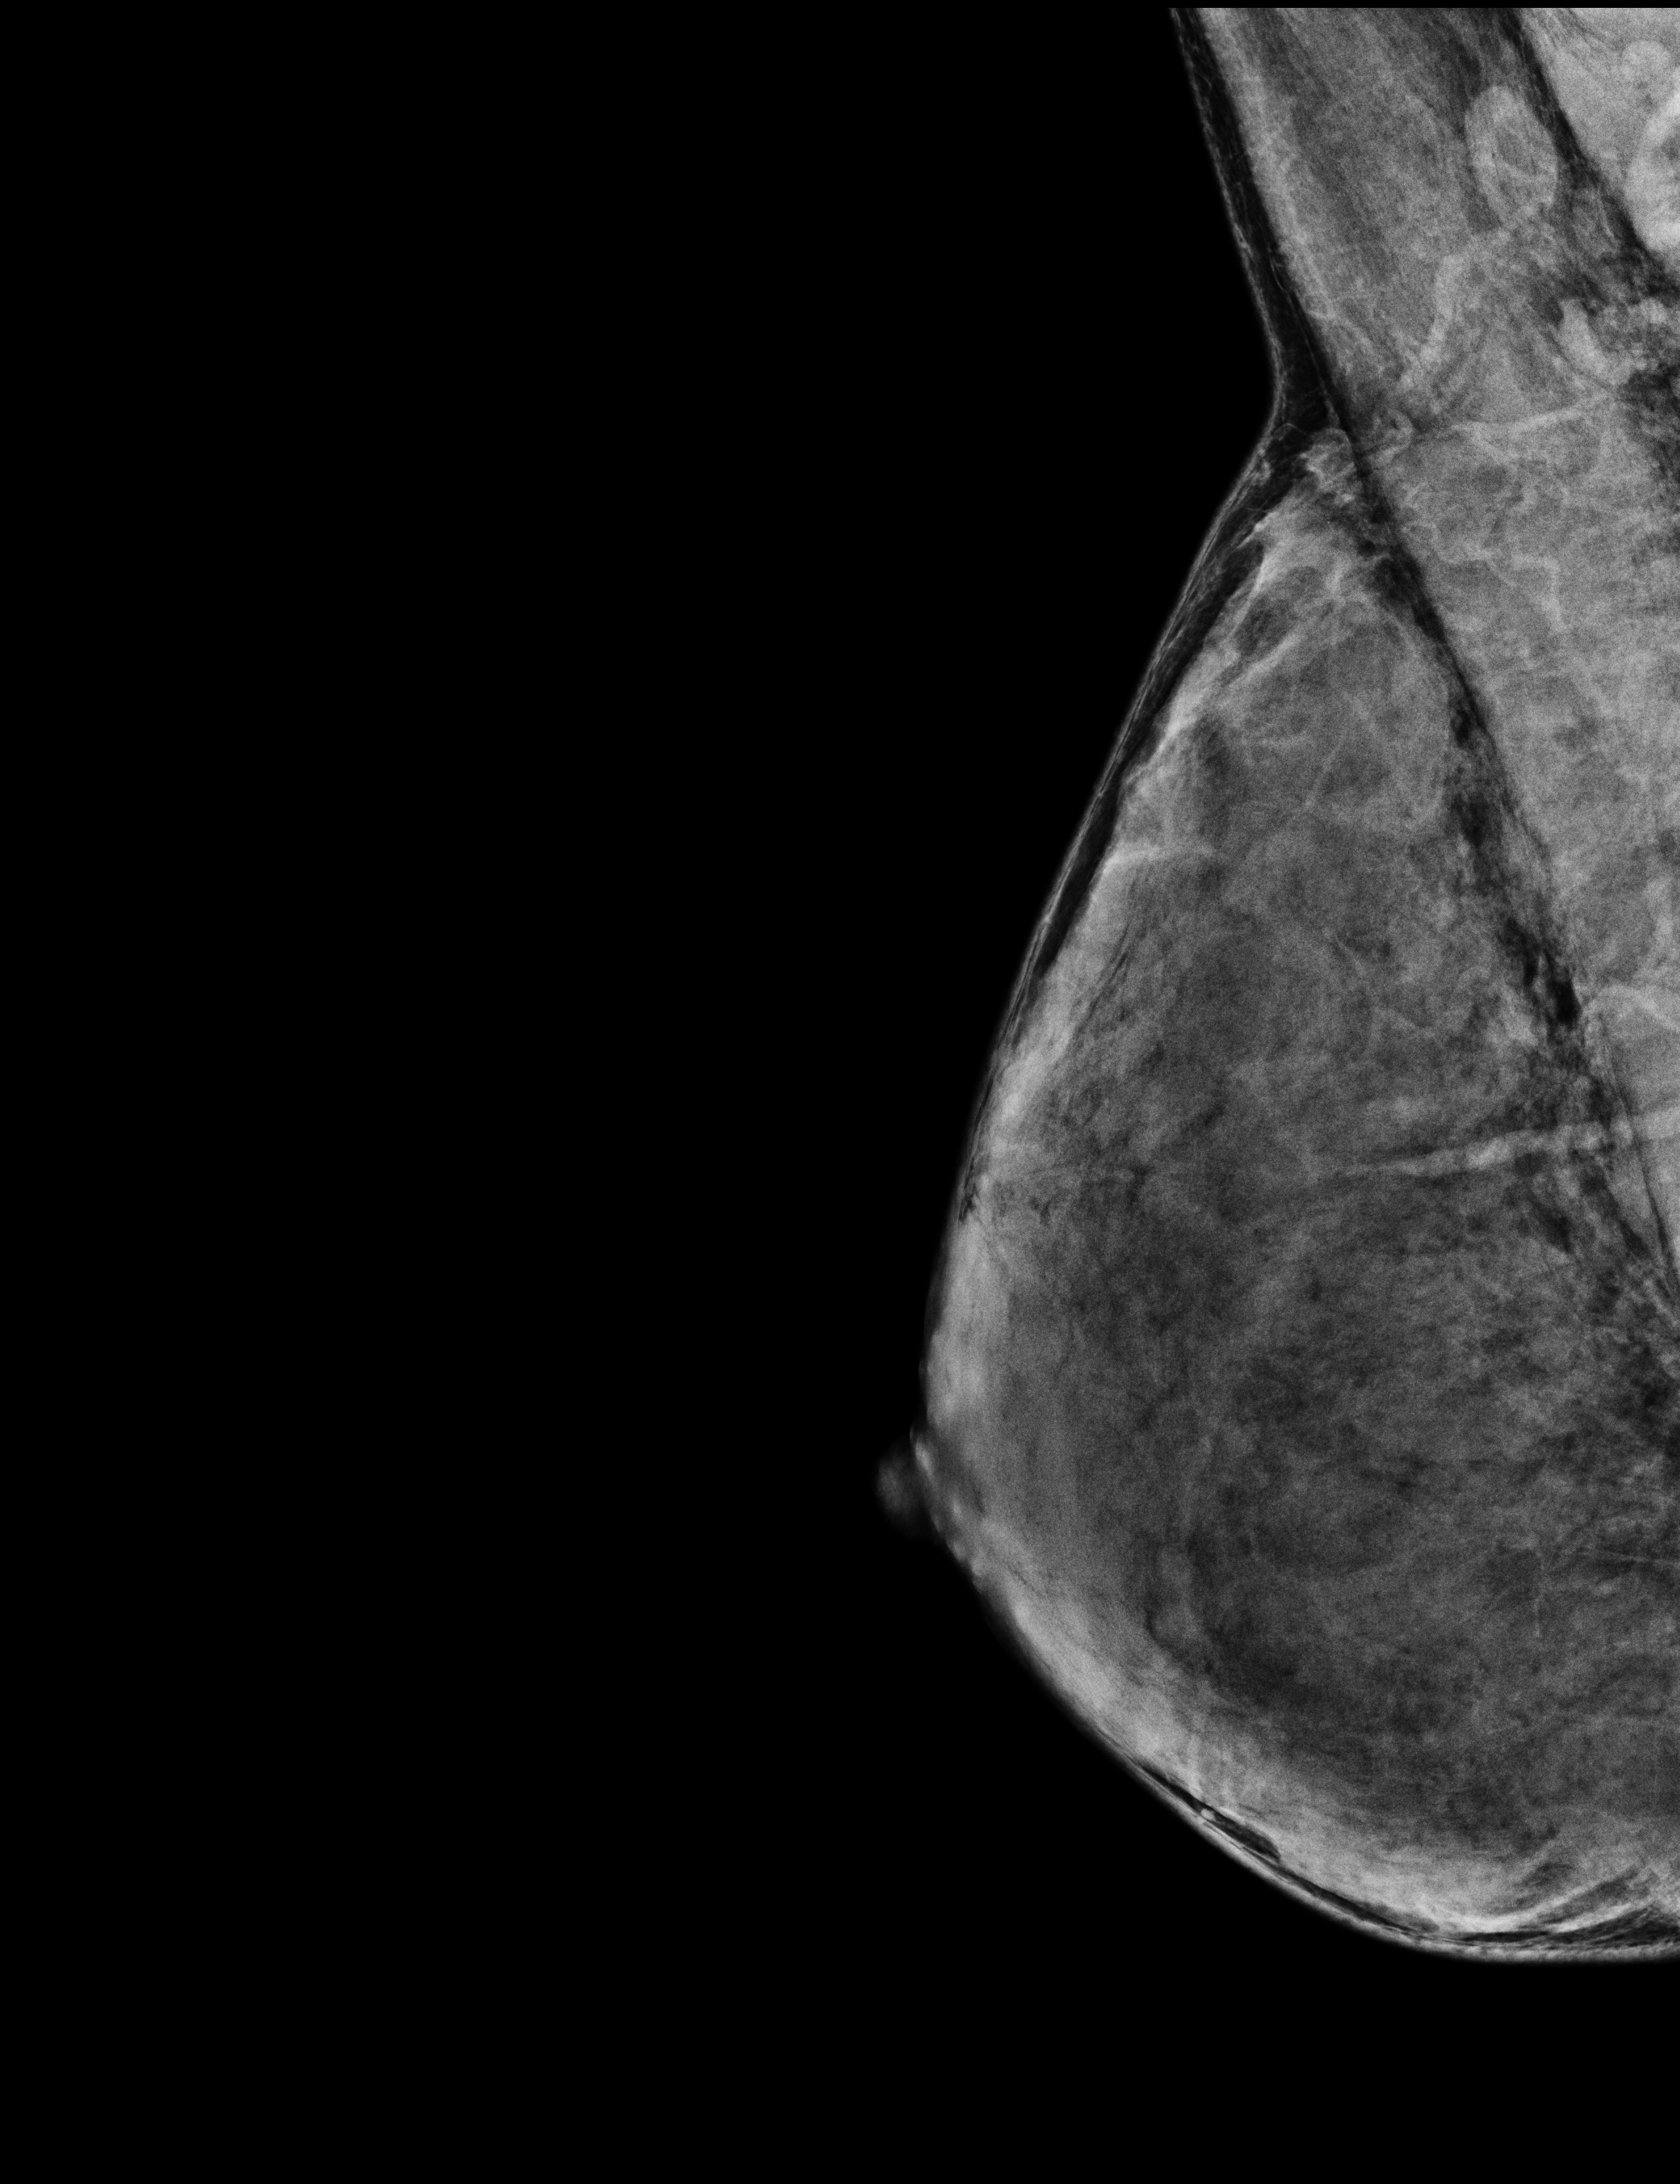
Screening examination, system: Selenia Dimensions. Patient aged 54 years (female).
Image type: full-field digital mammogram. Breast: right. Projection: MLO view. BI-RADS breast density category at the screening exam (both breasts, scale 1–4): 4. Final BI-RADS assessment for this screening round (tomosynthesis exam, both breasts): category 1. Recall: no recall after this screen.